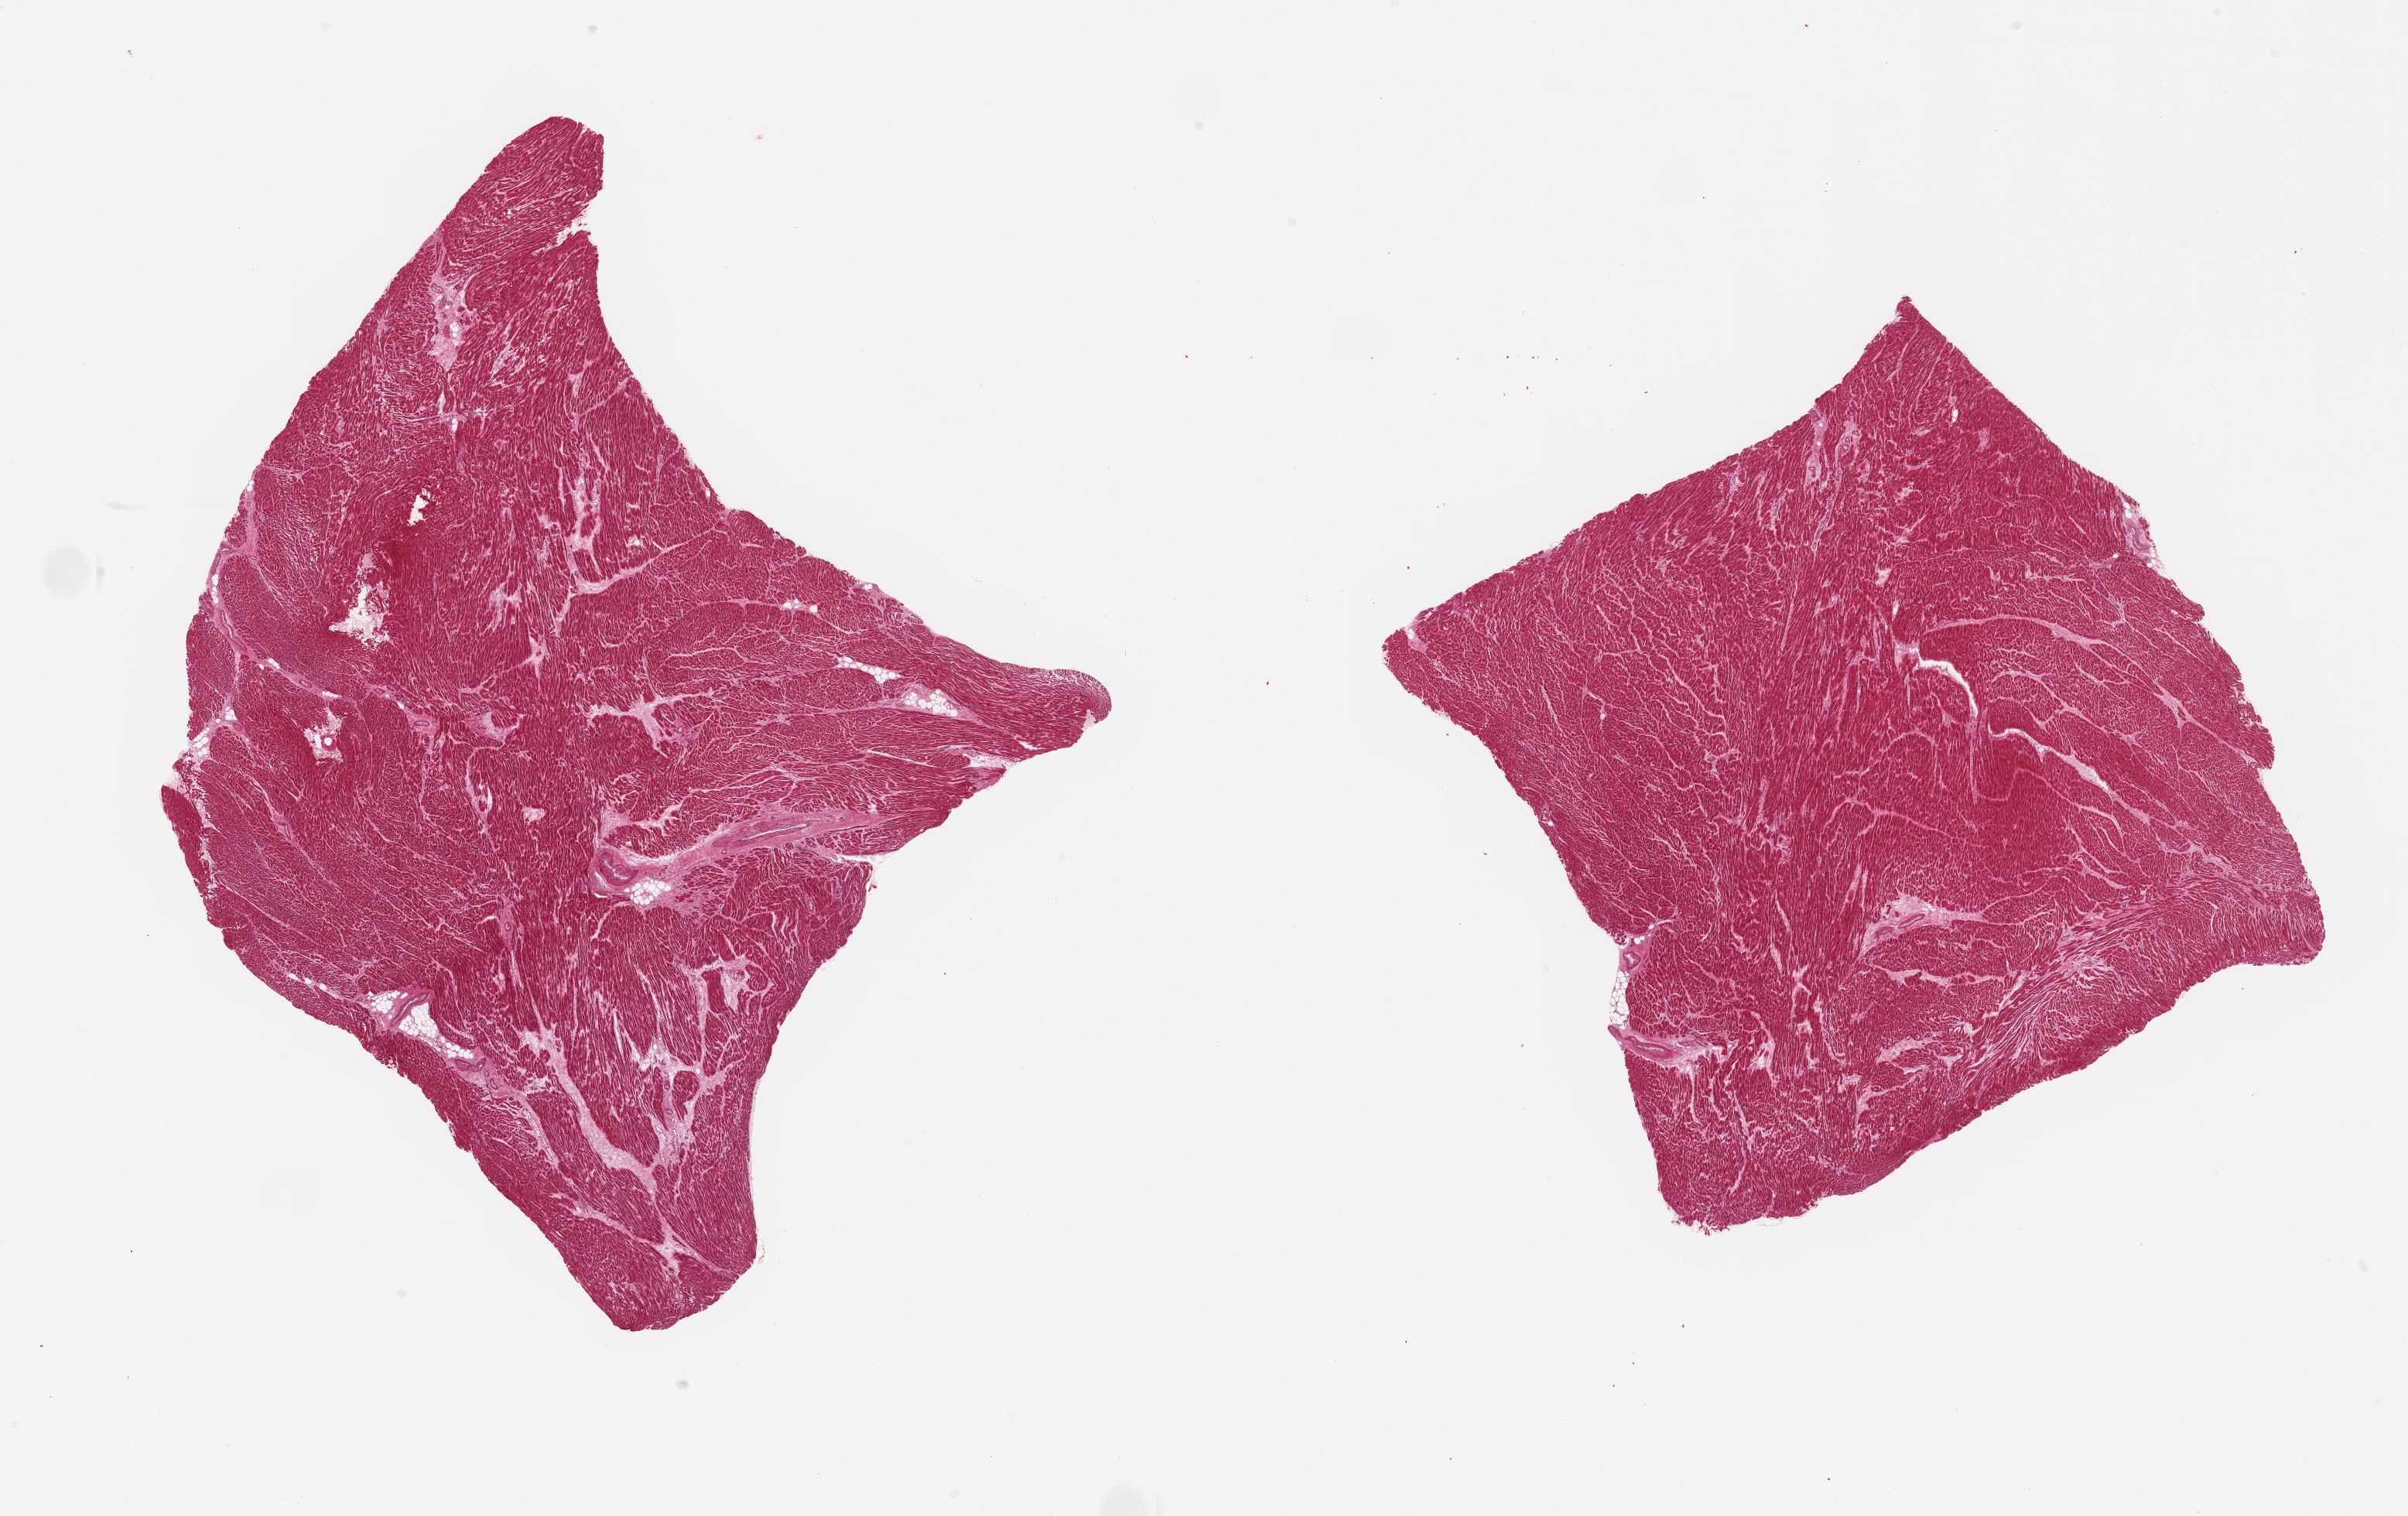
Whole-slide image, H&E stain, brightfield, shown as a low-resolution overview of the whole scanned area (about 24.6 x 15.5 mm, from a 20x scan), PAXgene-fixed paraffin-embedded (PFPE) section, sampled site (target tissue): heart, tissue donor sample. Donor sex: female.
Reviewer comment on this tissue sample: 2 pieces; patchy hypereosinophilia may indicate early ischemia.